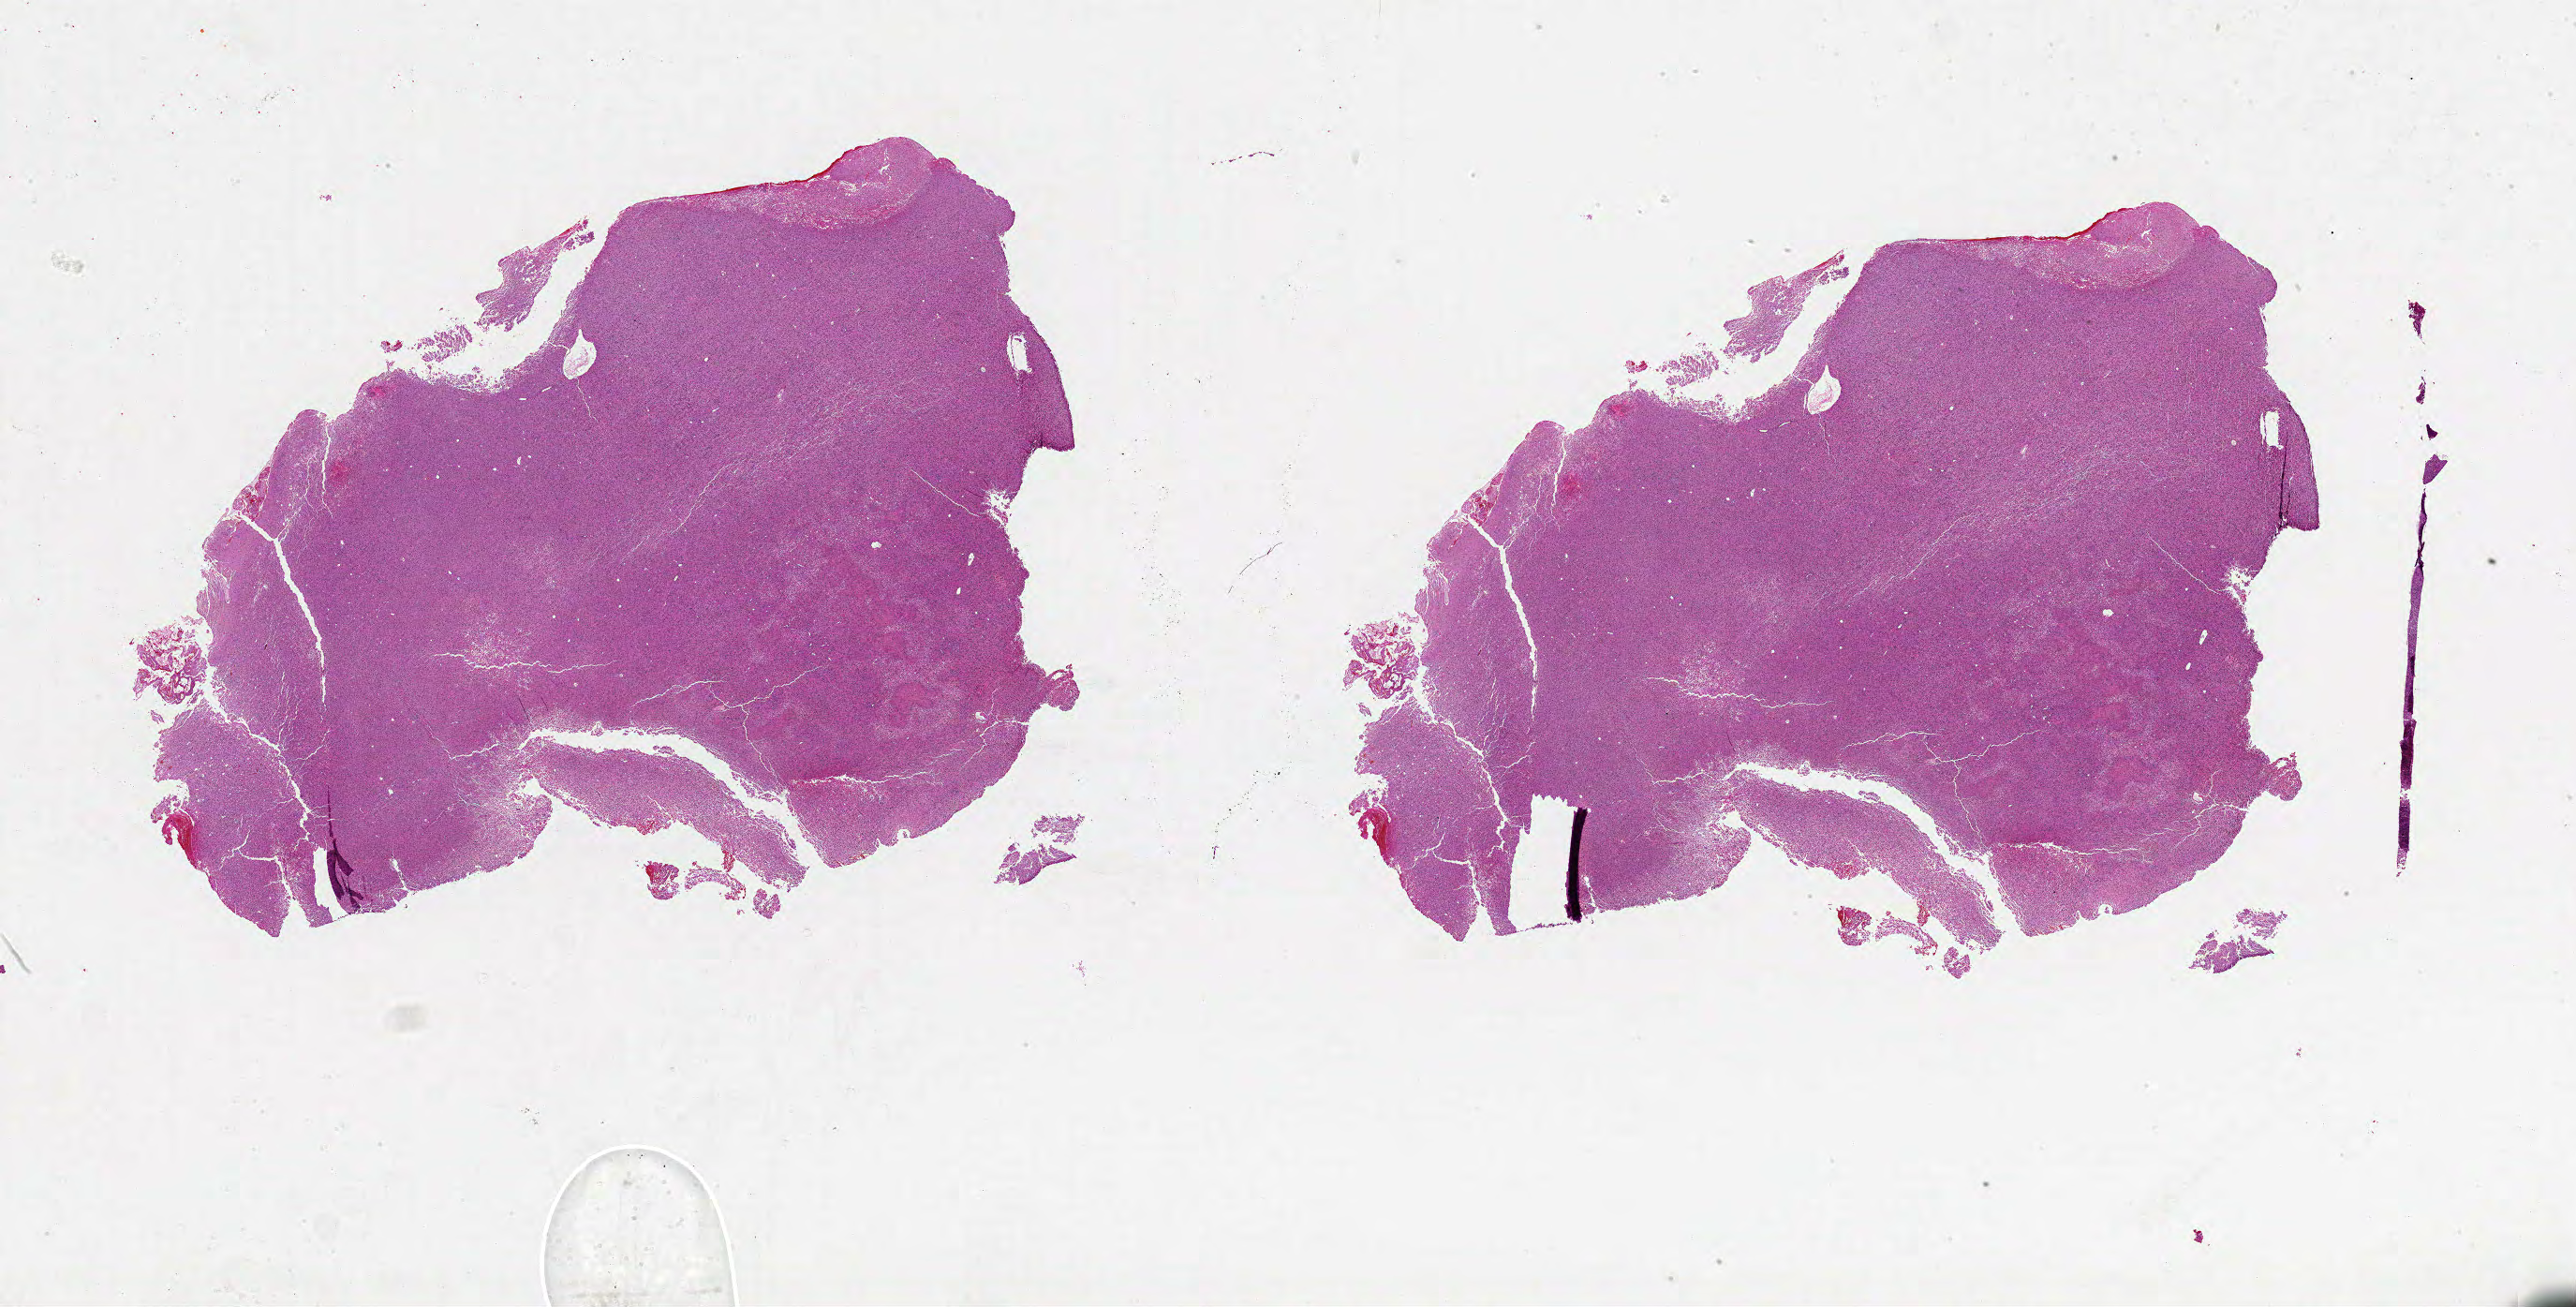
Whole-slide histology image, H&E-stained — low-resolution overview of the scanned area, about 44.0 x 22.3 mm (from a 20x scan); FFPE section; sample: primary tumour, brain. Female patient; age at initial diagnosis 66 years.
Histologic diagnosis: Glioblastoma.